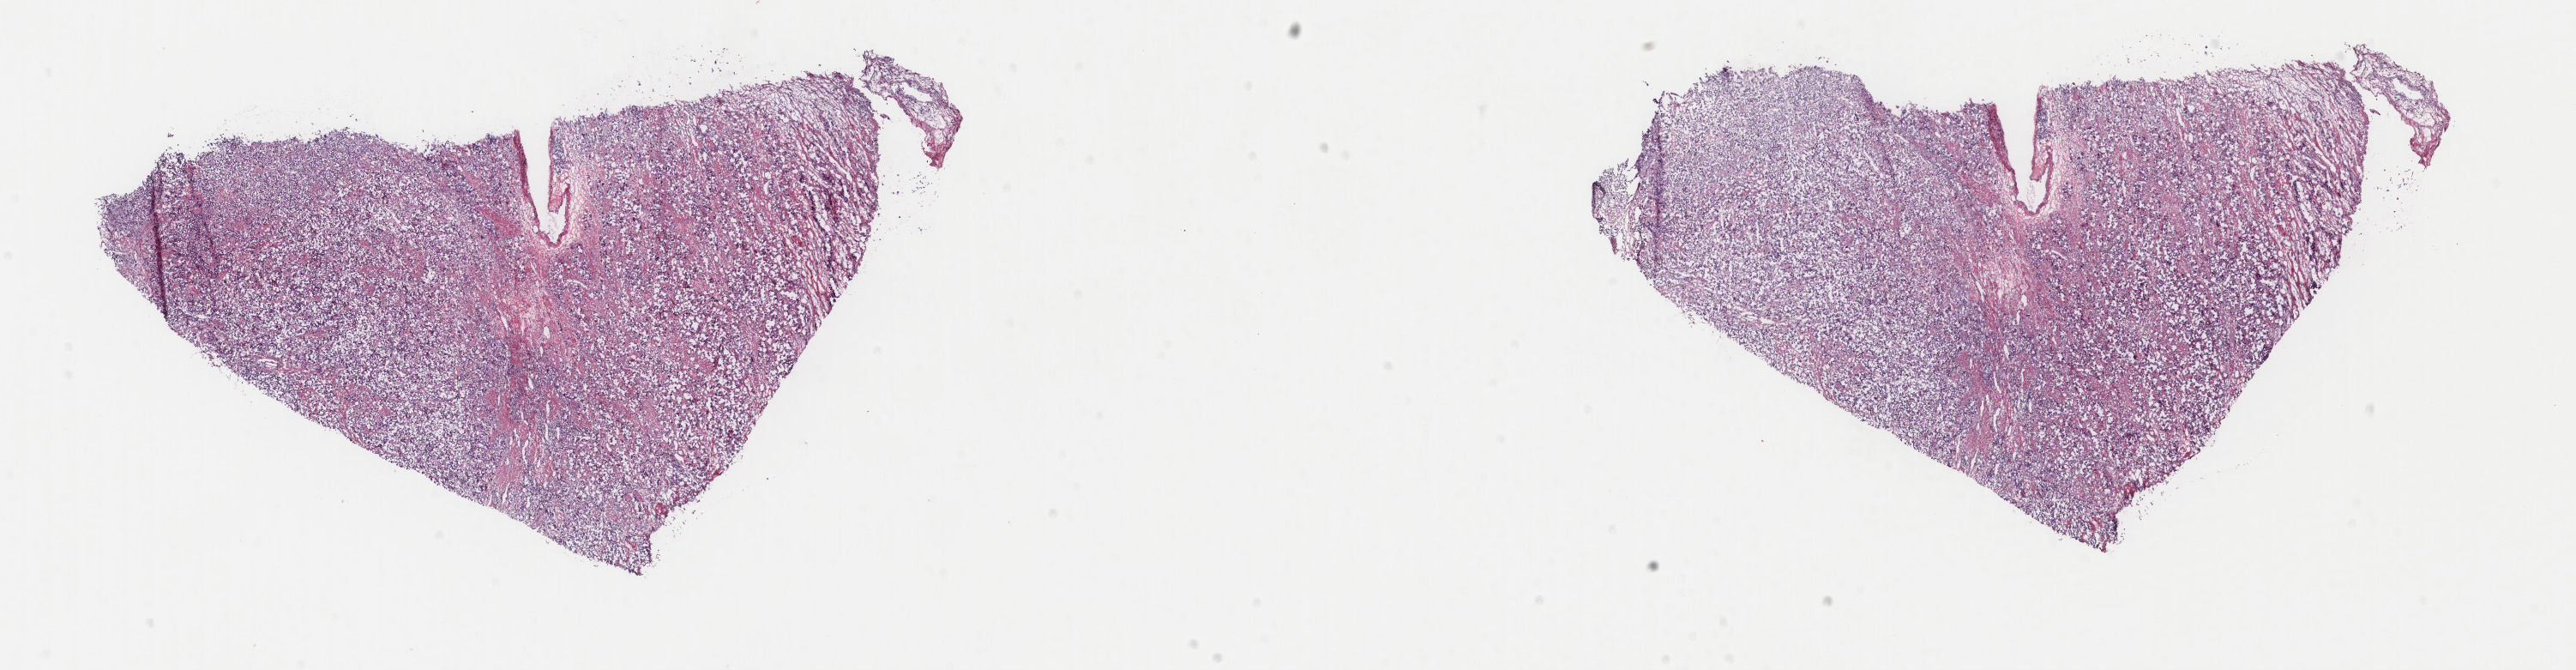
Whole-slide histology image, H&E, whole scanned area (about 23.8 x 6.2 mm) shown as a low-resolution overview, frozen section from the top of the tissue portion, bladder, primary tumour sample. Patient: male, age at initial diagnosis 83 years. Histologic grade: high grade. Composition of this section per pathologist review: tumour cells 100%, tumour nuclei 65%, normal cells 0%, stromal cells 0%, necrosis 0%. Infiltration values recorded for this section: lymphocyte infiltration 4%, monocyte infiltration 0%, neutrophil infiltration 0%.
* lymph nodes positive (case pathology): 2 of 2 examined
* AJCC pathologic stage: IV (7th edition)
* pathologic diagnosis: Transitional cell carcinoma